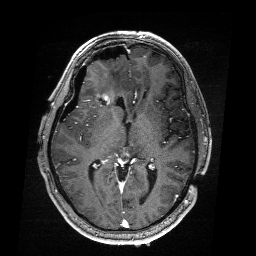
Brain MRI from a brain-tumour surgery series, one axial slice; slice 106 of 176 in the series (ordered by position); T1-weighted post-contrast; 1 mm slice thickness; 256 × 256 image matrix, field of view 256 × 256 mm. From the clinical record (not read from this slice): histopathology: Astrocytoma; WHO grade: 4; IDH mutation: yes; tumour location: Right Frontal.
Outlined on this slice (manually delineated by an expert):
- residual tumour: bounding box <90,88,119,99> (left, top, right, bottom; pixels)